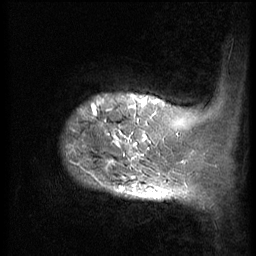
Breast MRI (dynamic contrast-enhanced), one sagittal slice; position 6 of 56 along the scan axis; 3 images stored at this slice position (order not interpretable as contrast timing); 1.5 T; TE 4.2 ms, TR 9 ms; 256 × 256 image matrix, field of view 180 × 180 mm. Female patient, age 49 years. From the clinical record (not read from this slice): setting: breast cancer imaged before/during neoadjuvant chemotherapy; receptor status: HER2-positive.
Structures marked on this image (semi-automatically segmented with operator editing):
- analysis volume of interest (the breast-tissue region the enhancement analysis was run in; not a lesion): bounding box <59,85,168,207> (left, top, right, bottom; pixels)
- tumour enhancement mask (voxels above the 140 % enhancement threshold inside the analysis volume of interest): <69,98,161,198>